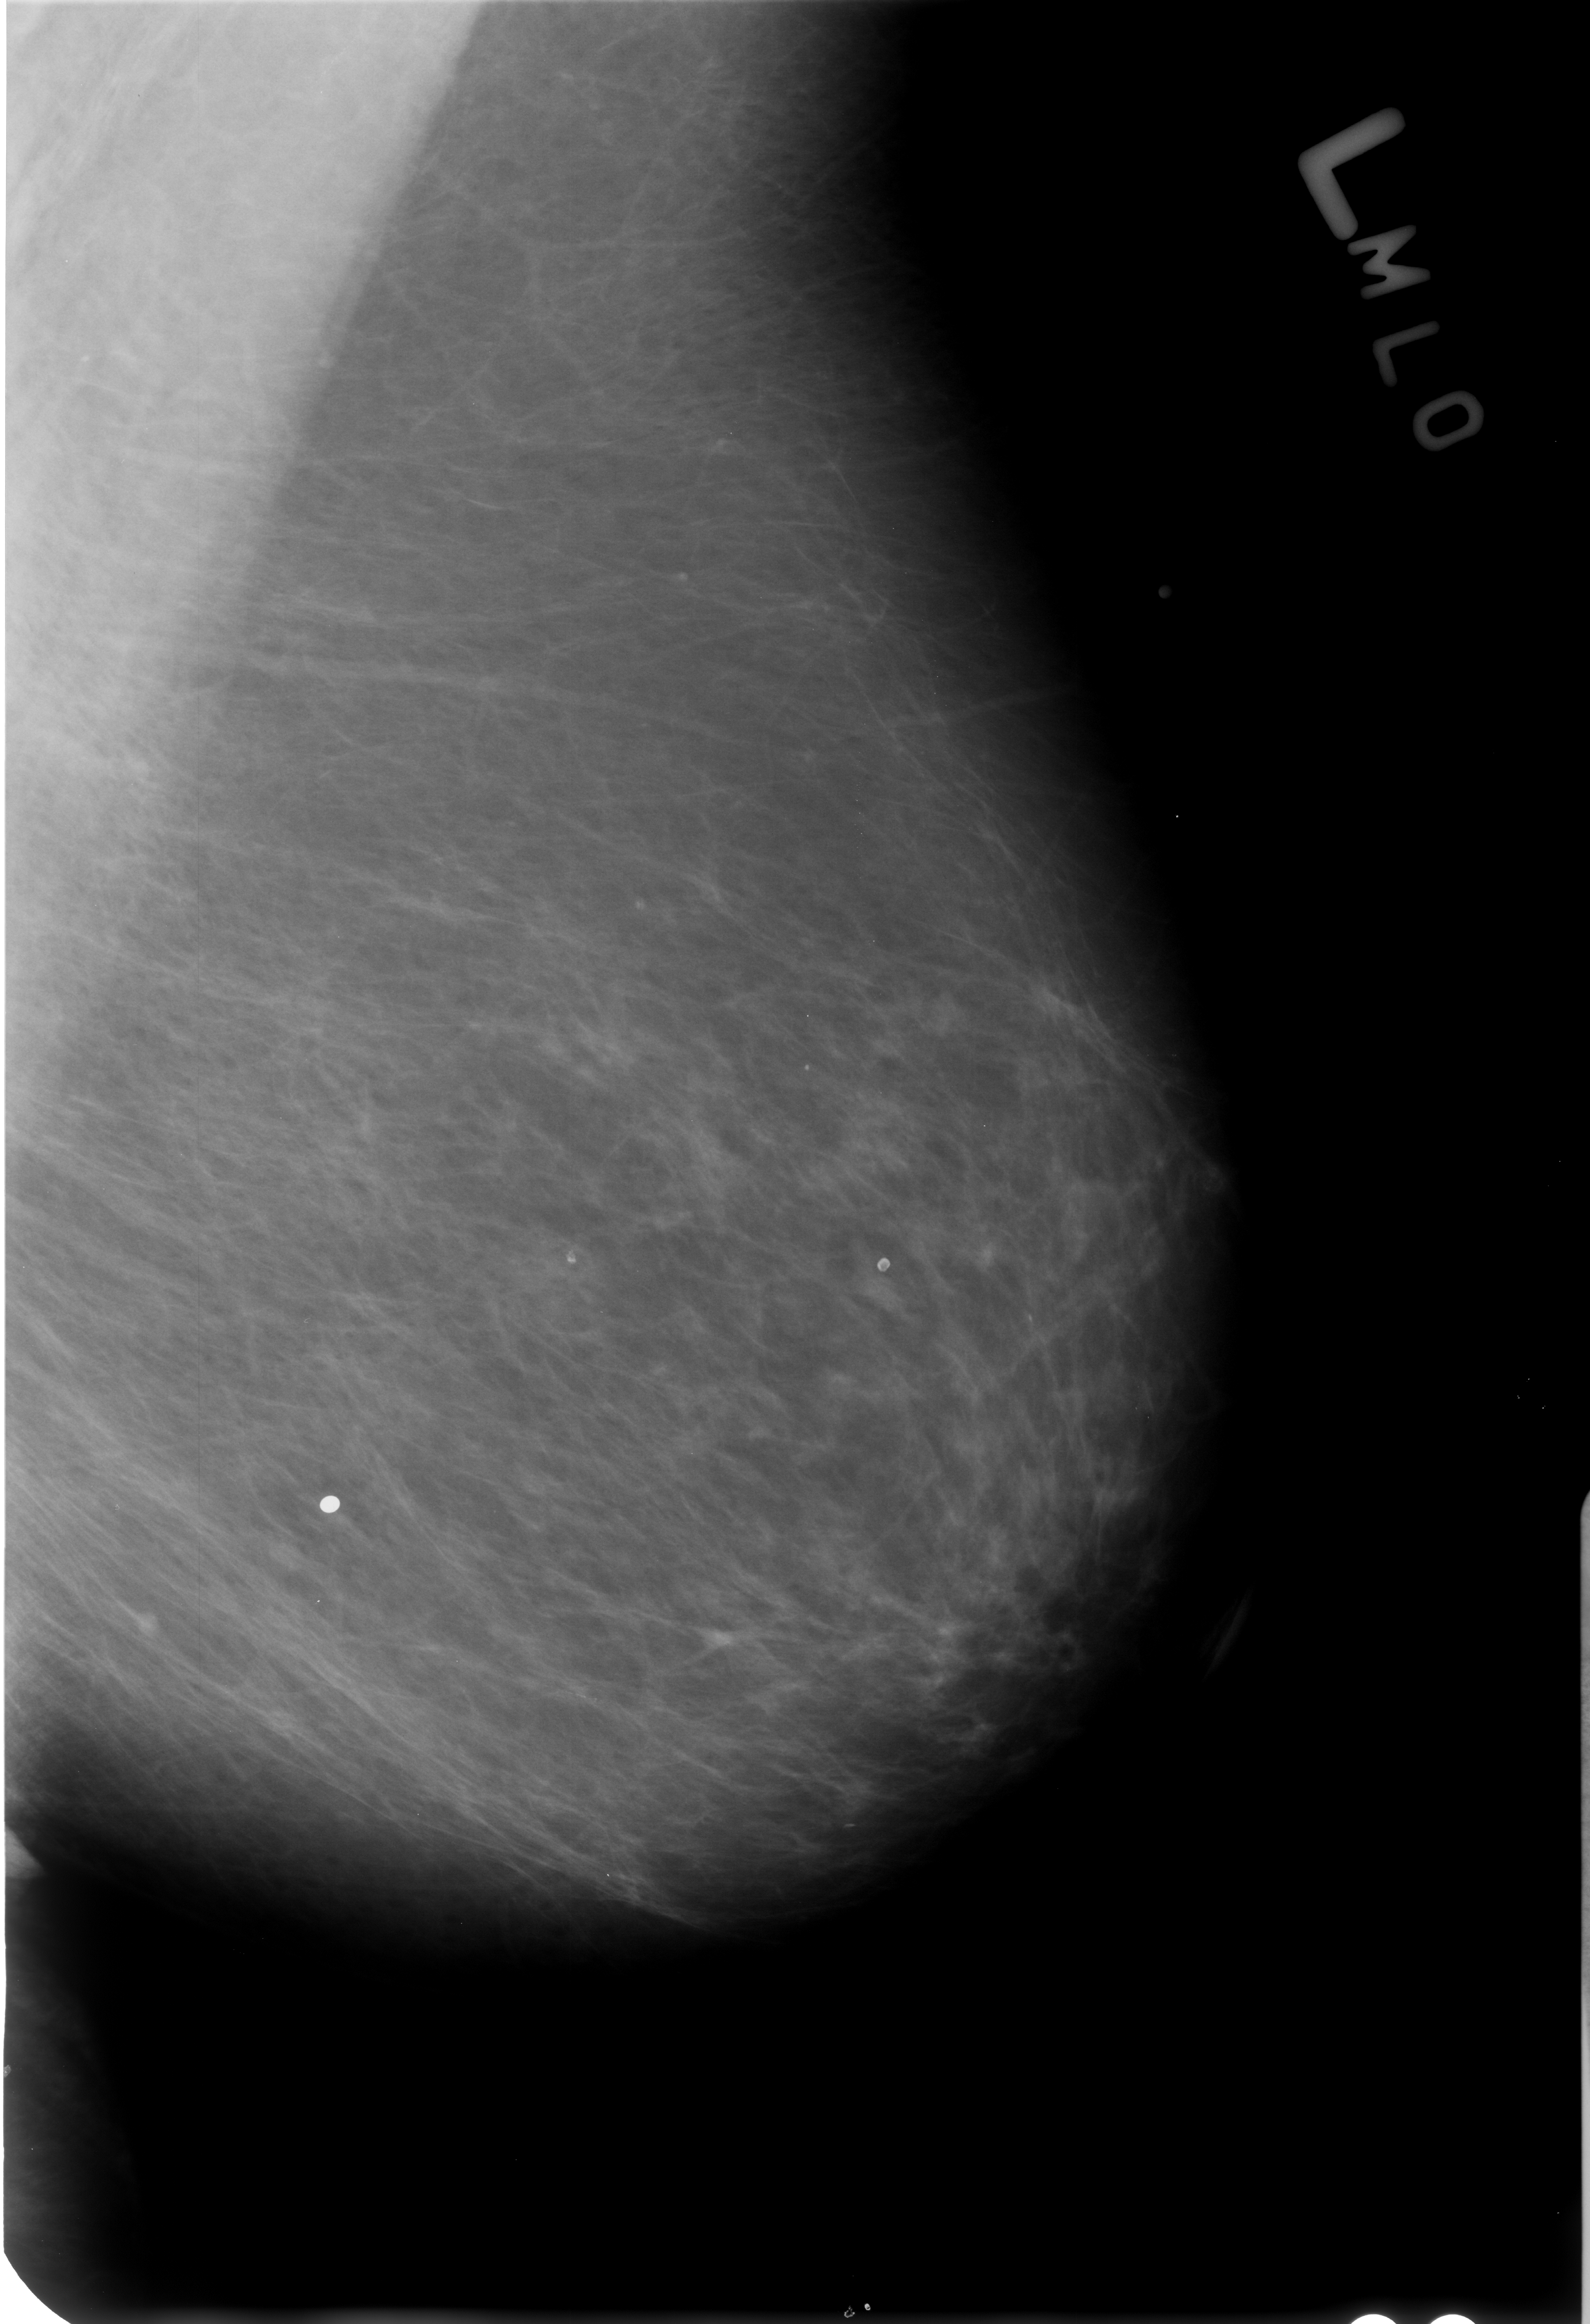
Mammogram (digitized film); left breast; mediolateral oblique (MLO) view; BI-RADS breast density category 1 (scale 1–4).
Radiologist-marked abnormalities on this image: Finding 1 of 2: calcifications, morphology lucent center; BI-RADS assessment category 2; benign without callback (not worked up further). Finding 2 of 2: calcifications, morphology lucent center; BI-RADS assessment category 2; benign without callback (not worked up further).